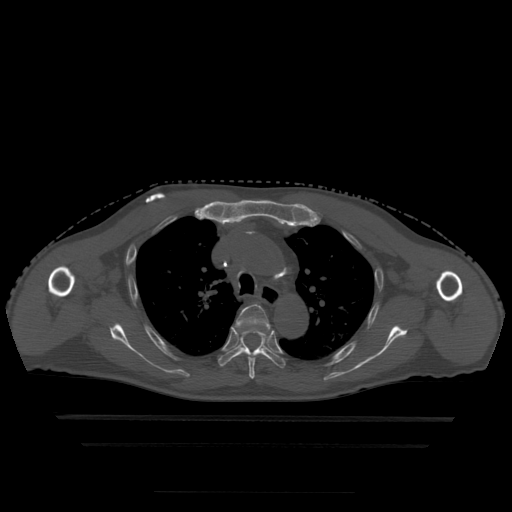
CT including the spine, one axial slice; slice 345 of 522 in the series (ordered by position); bone window (W 1800 / L 400 HU); 1.25 mm slice thickness; 512 × 512 image matrix. Patient age 68 years. Case-level facts recorded for this patient, not image findings: primary cancer: urothelial.
Annotated regions visible in this slice (semi-automatically segmented with operator editing):
- T4 vertebra: box from (x=236, y=305) to (x=270, y=379) px
- T5 vertebra: (x=219, y=324)–(x=286, y=368)